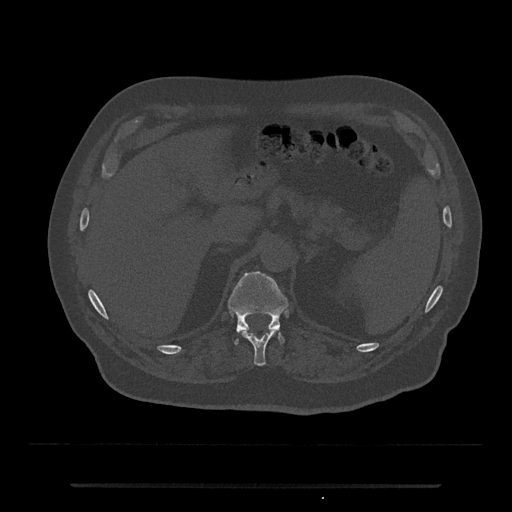
CT including the spine, one axial slice; slice 618 of 797 in the series (ordered by position); reconstruction kernel Br40s/3; bone window (W 1800 / L 400 HU); 0.5 mm slice thickness; 512 × 512 image matrix. Male patient, age 80 years. From the clinical record (not read from this slice): primary cancer: prostate; vertebrae with lytic lesions (as recorded): L1, T11.
Structures marked on this image (semi-automatic segmentation, software-assisted and operator-edited):
- T11 vertebra: box from (x=242, y=329) to (x=276, y=366) px
- T12 vertebra: (x=228, y=271)–(x=288, y=345)